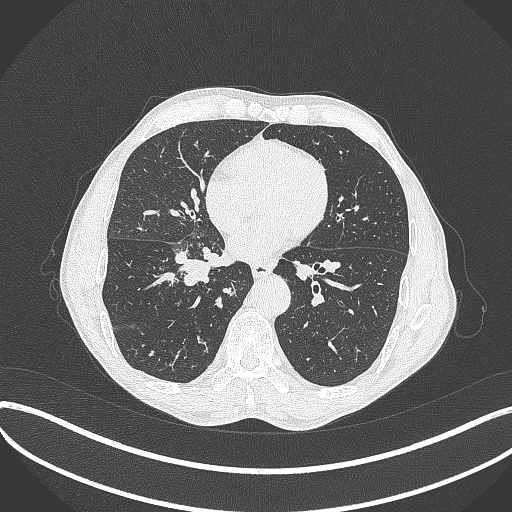
Chest CT, one axial slice. Position 184 of 481 along the scan axis. Reconstruction kernel B70f. 120 kVp. Lung window (W 1500 / L -600 HU). 1 mm slice thickness. 512 × 512 image matrix, field of view 400 × 400 mm. Patient: male, 65 years. From the clinical record (not read from this slice): clinical TNM (as recorded): T2a N0 M0.
Annotated regions visible in this slice (bounding box drawn by a radiologist):
- lung tumour (recorded histology: squamous cell carcinoma): bounding box [x1, y1, x2, y2] px = [173, 248, 237, 293]